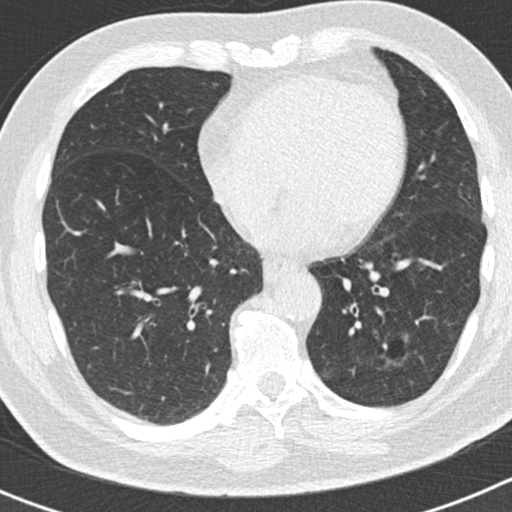
Low-dose screening chest CT, axial slice; second screening round (one year after baseline); lung window (W 1500 / L -600 HU); 2 mm slice thickness; standard (soft-tissue) reconstruction kernel (B30f); slice 104 of 186 in the series. Male, age 66 years at enrolment. Former smoker at enrolment.
Expert-annotated lung lesion, bounding box (x1, y1, x2, y2) in pixels: (344, 320, 418, 402). Screening reader's record for this exam (one nodule recorded; not confirmed to be the boxed lesion): non-calcified nodule or mass ≥4 mm, left lower lobe, 50 × 33 mm, smooth margins, pre-existing on the prior screen: yes; interval growth: yes. Later outcome: lung cancer diagnosed 440 days after this screen — adenocarcinoma, NOS, left lower lobe, poorly differentiated (G3), stage IB (AJCC 6th edition), 38 mm at pathology.